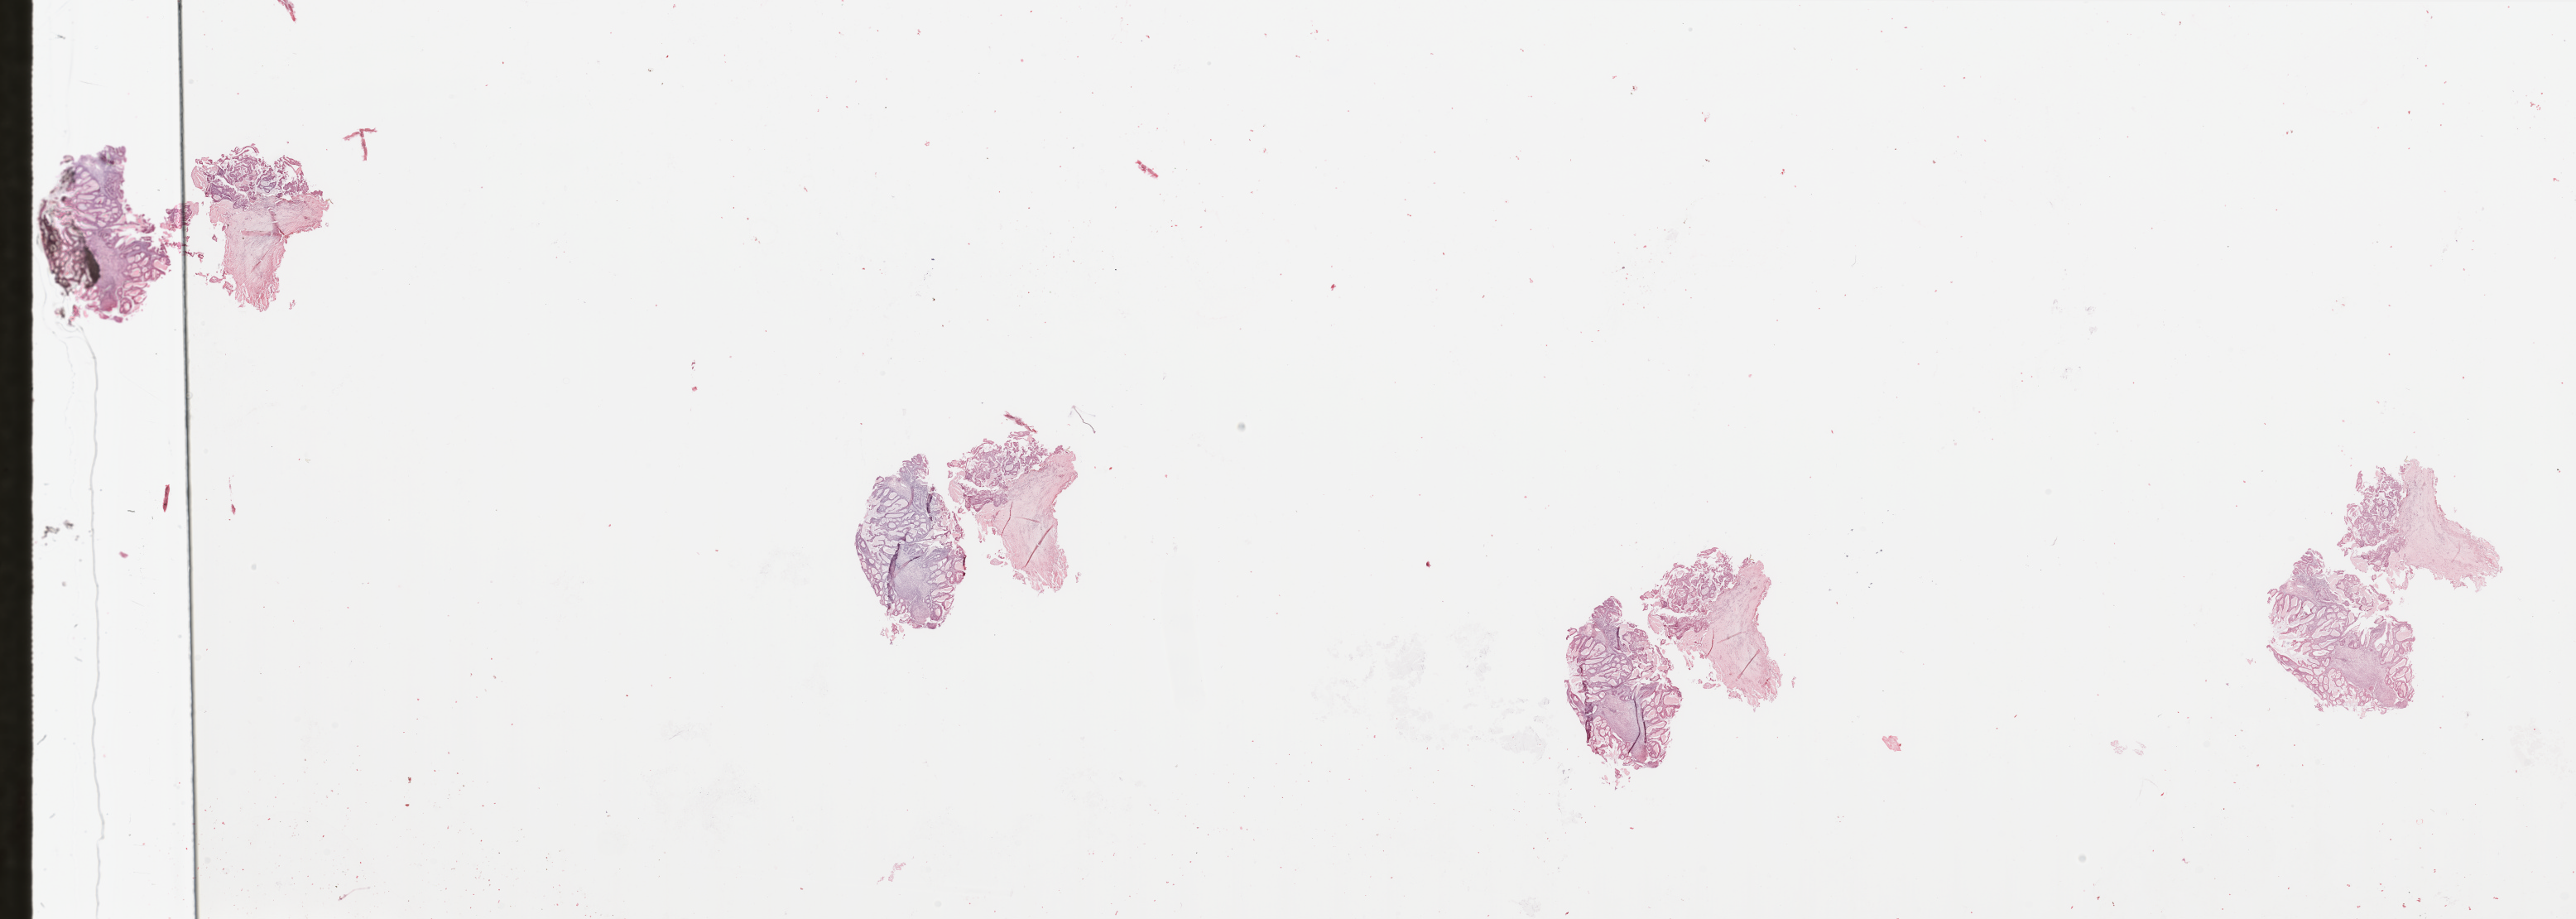
H&E-stained whole-slide image, a low-resolution overview of the entire scanned area, about 49.2 x 17.6 mm, uterus, tumour tissue. Patient: female, age 60 years. Histologic grade: G2 (moderately differentiated).
Primary tumour site (as recorded): anterior endometrium. Diagnosis: Endometrioid adenocarcinoma, NOS. AJCC pathologic stage: IIIB.